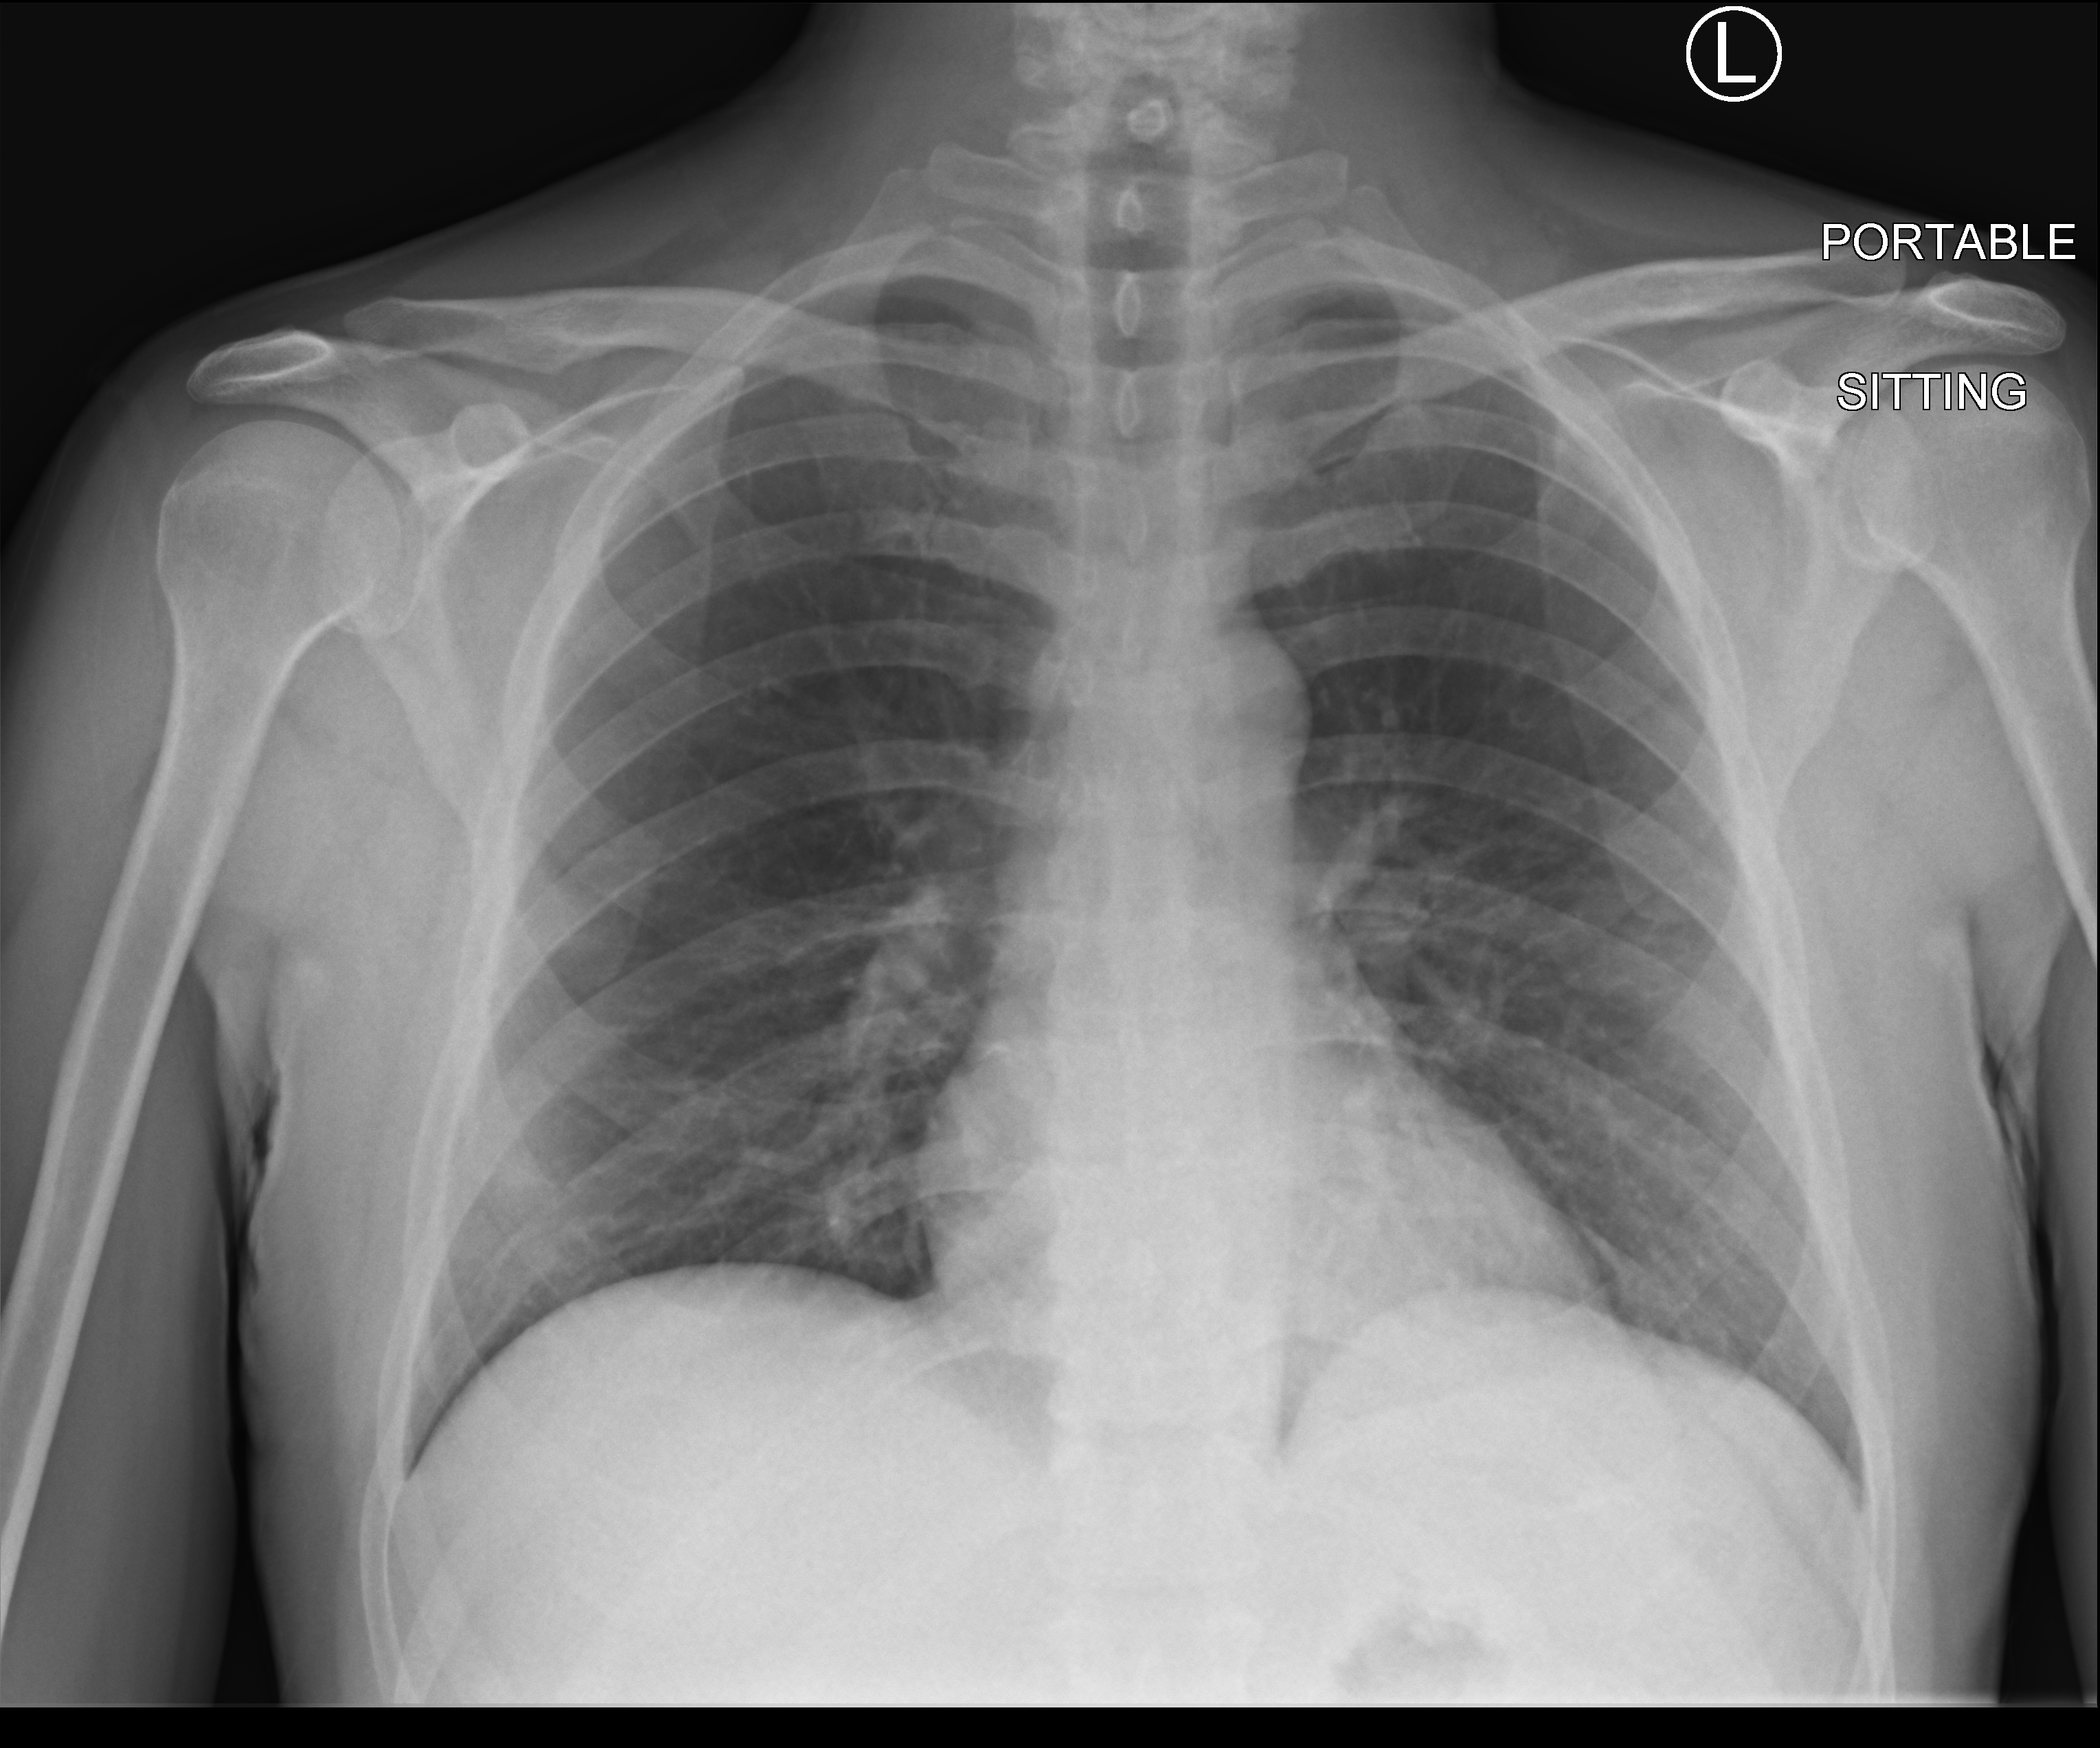
Bedside chest radiograph (computed radiography); anteroposterior (AP) projection. Male patient hospitalised with COVID-19, age 18–59 years.
Hospital-stay facts (about this admission, not read from this image; timing relative to this image not recorded): diabetes (admission record): no; admitted to intensive care during this hospital stay: no; mechanically ventilated during this hospital stay: no.